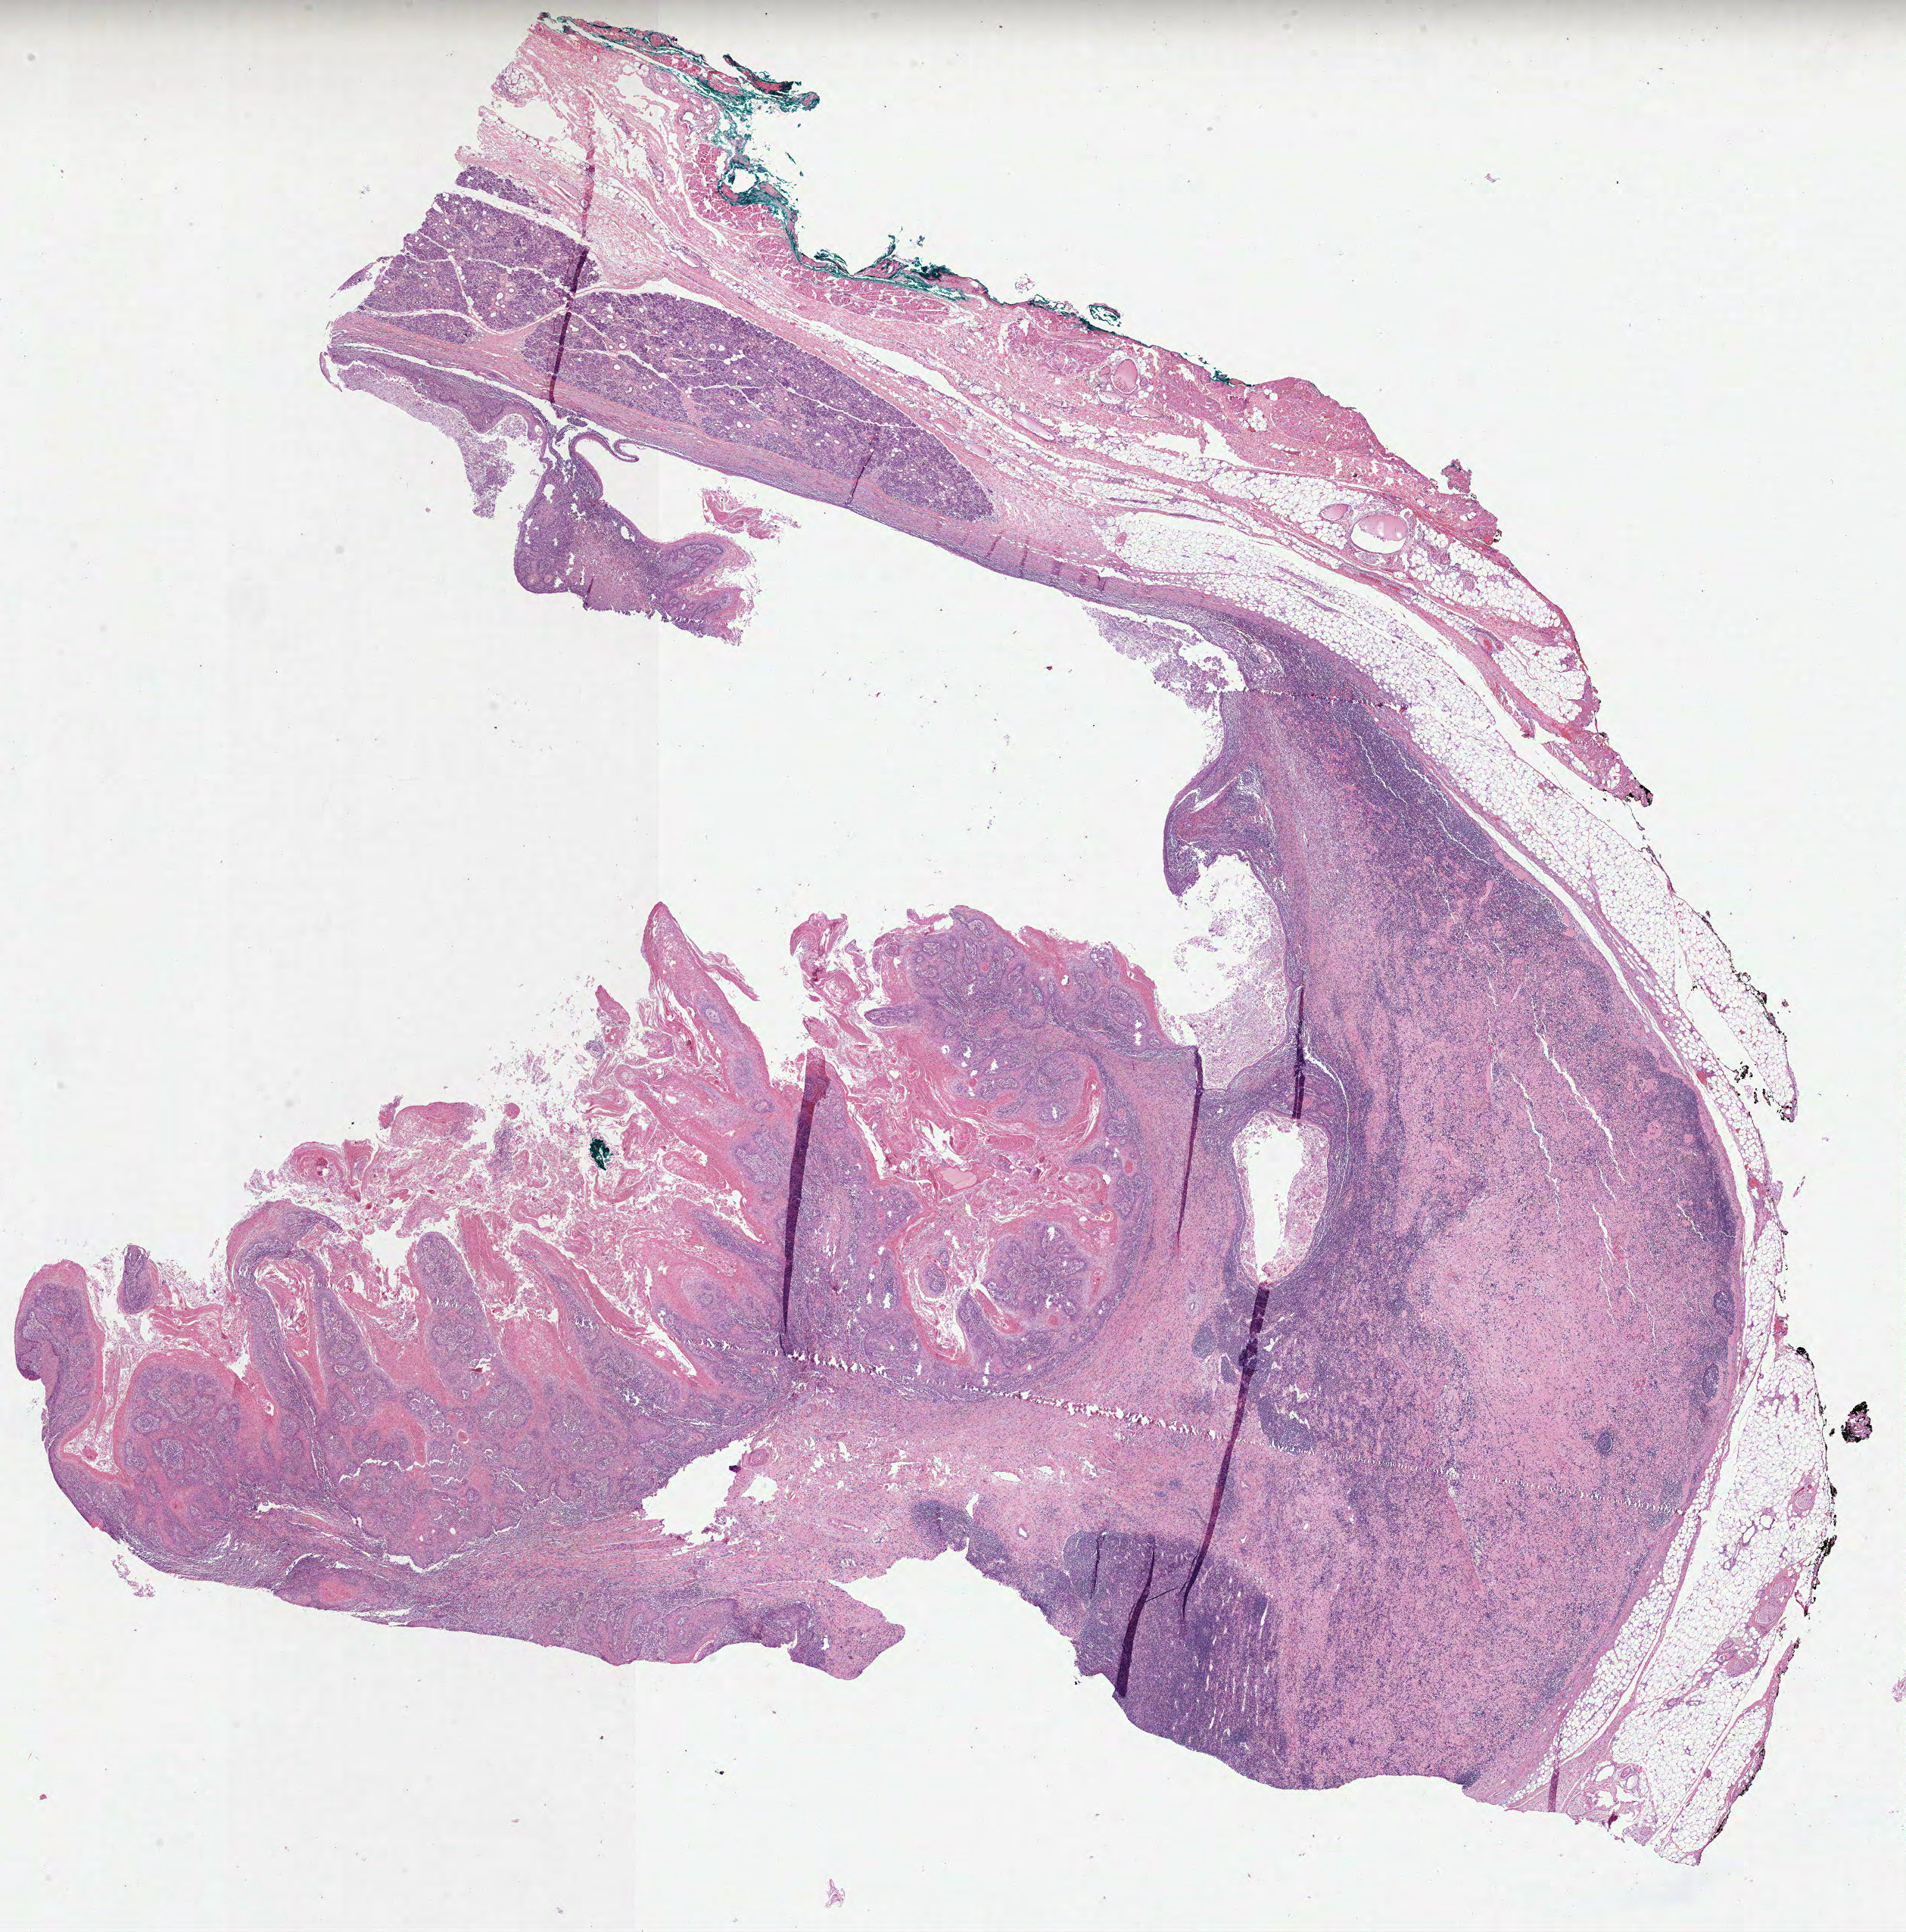
H&E-stained whole-slide image, shown as a low-resolution overview of the whole scanned area (about 20.3 x 20.6 mm, slide scanned at 40x), formalin-fixed paraffin-embedded (FFPE) diagnostic section, head and neck, primary tumour sample. Patient: female, age at initial diagnosis 41 years. Histologic grade: G1 (well differentiated).
• diagnosis: Squamous cell carcinoma, NOS (cheek mucosa)
• AJCC pathologic stage: IVA (7th edition)
• laterality: left